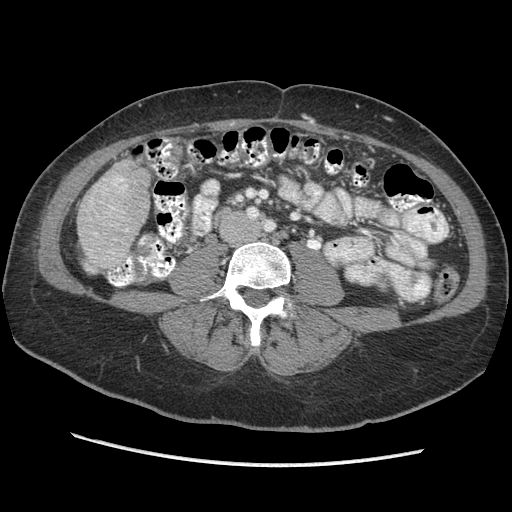
Contrast-enhanced abdominal CT (liver protocol), one axial slice; position 87 of 170 along the scan axis; reconstruction kernel STANDARD; soft-tissue window (W 400 / L 40 HU); 2.5 mm slice thickness; 512 × 512 image matrix, field of view 360 × 360 mm. From the clinical record (not read from this slice): diagnosis: hepatocellular carcinoma (patient treated with transarterial chemoembolisation; whether this scan precedes or follows treatment is not stated here); TNM stage (as recorded): Stage-II; Child-Pugh class: A; tumour differentiation: no biopsy; tumour nodularity: multinodular.
Structures marked on this image (semi-automatically segmented with operator editing):
- liver parenchyma outside the tumour (the mass and vessels are separate outlines, so this box may not span the whole liver): bounding box <76,160,150,271> (left, top, right, bottom; pixels)
- liver vessels: <95,178,127,234>